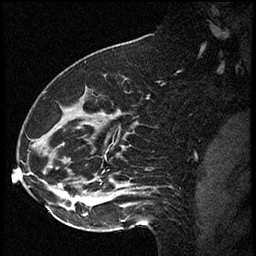
Breast MRI (dynamic contrast-enhanced), one sagittal slice. Position 23 of 60 along the scan axis. Dynamic contrast-enhanced series, image 2 of 2 at this slice position (ordered by acquisition). 1.5 T. TE 4.2 ms, TR 17.3 ms. 256 × 256 image matrix, field of view 200 × 200 mm. Female patient. From the clinical record (not read from this slice): setting: breast cancer imaged before/during neoadjuvant chemotherapy; receptor status: HR-positive, HER2-negative.
Annotated regions visible in this slice (semi-automatically segmented with operator editing):
- analysis volume of interest (the breast-tissue region the enhancement analysis was run in; not a lesion): bounding box <41,93,115,223> (left, top, right, bottom; pixels)
- tumour enhancement mask (voxels above the 100 % enhancement threshold inside the analysis volume of interest): <72,197,84,201>